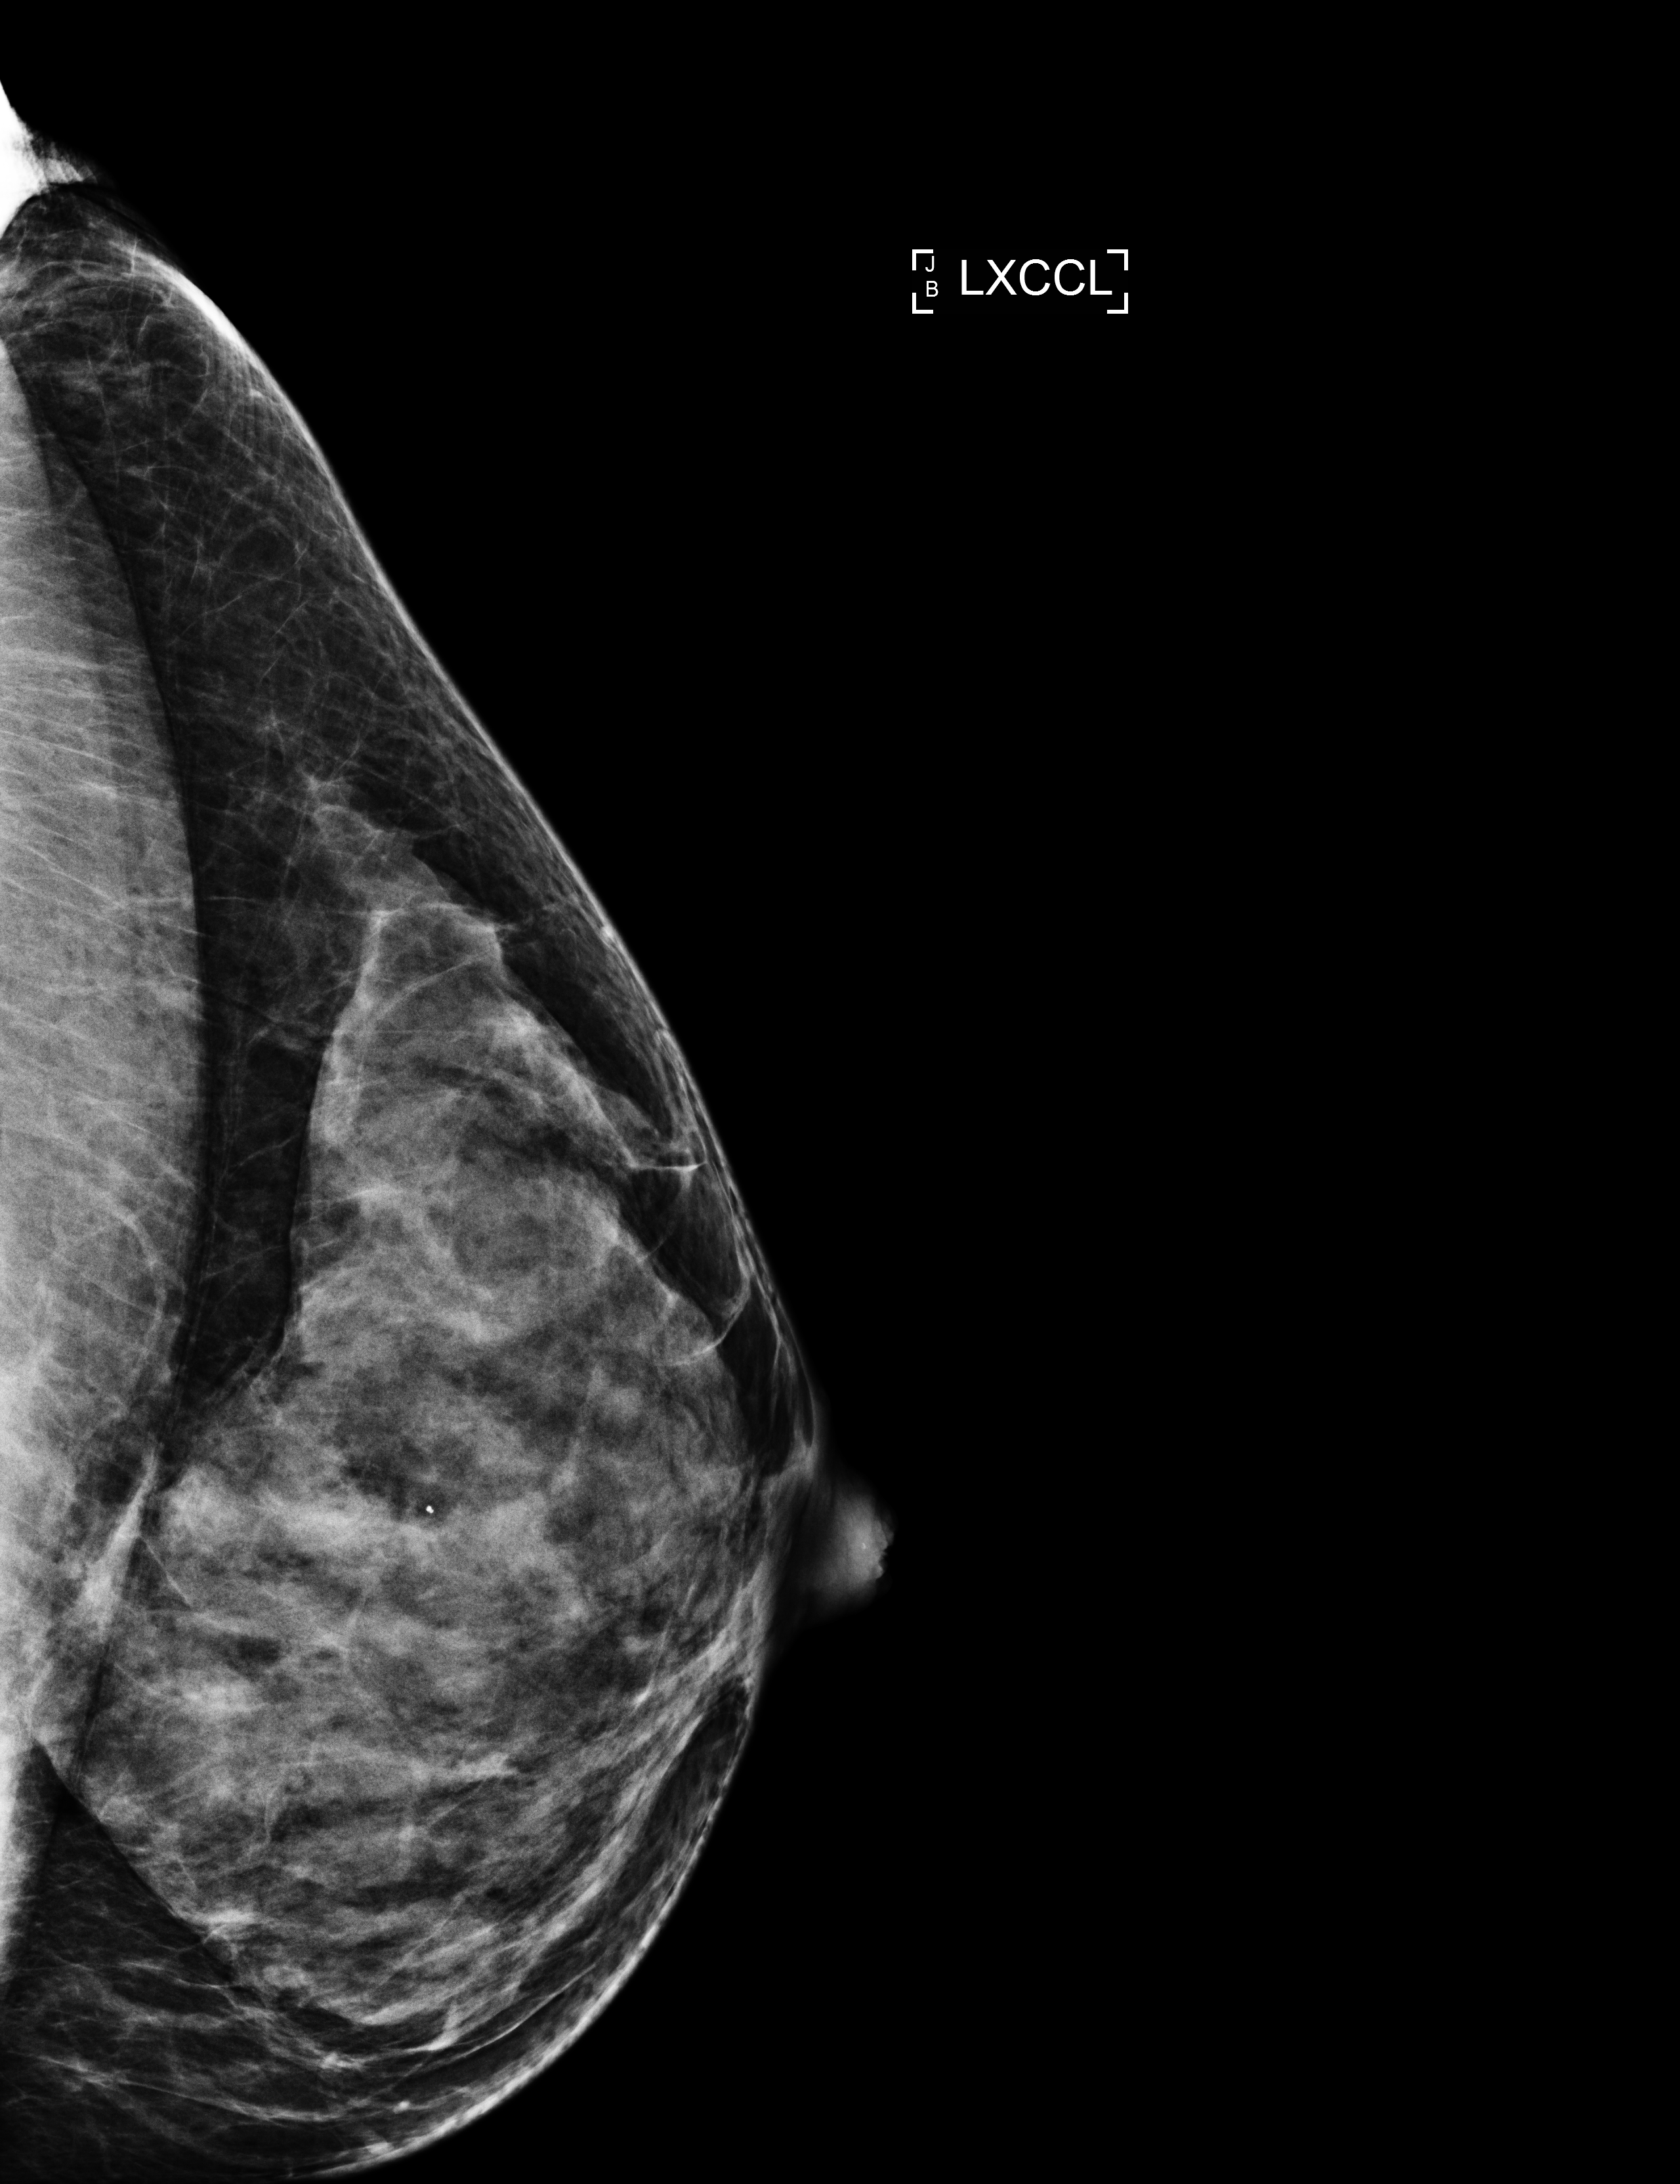
Annual screening mammography examination, compressed breast thickness 46 mm. Female patient, age 47 years.
Image type: full-field digital mammogram. Breast: left. Projection: laterally exaggerated craniocaudal (XCCL) view.